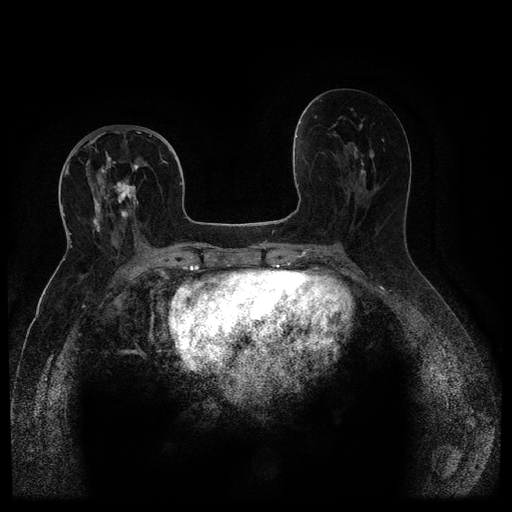
Breast MRI (dynamic contrast-enhanced, multi-phase), one axial slice. Slice 51 of 116 in the series (ordered by position). Dynamic contrast-enhanced series, time point 2 of 5 at this slice position (early post-contrast). 1.5 T. TE 2.6 ms, TR 5.4 ms. 2 mm slice thickness. 512 × 512 image matrix, field of view 340 × 340 mm. Patient: female, 68 years.
Annotated regions visible in this slice (semi-automatically segmented with operator editing):
- breast lesion (labelled 'tumour' in the annotation; benign lesions carry a separate 'benign' label): box from (x=113, y=178) to (x=139, y=206) px
- breast lesion (labelled 'tumour' in the annotation; benign lesions carry a separate 'benign' label): (x=91, y=190)–(x=104, y=236)